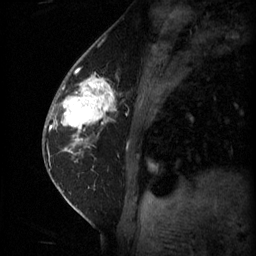
Breast MRI (dynamic contrast-enhanced), one sagittal slice; position 22 of 60 along the scan axis; 3 images stored at this slice position (order not interpretable as contrast timing); 1.5 T; TE 4.2 ms, TR 11 ms; 2 mm slice thickness; 256 × 256 image matrix, field of view 180 × 180 mm. Female patient, age 62 years.
Annotated regions visible in this slice (semi-automatically segmented with operator editing):
- analysis volume of interest (the breast-tissue region the enhancement analysis was run in; not a lesion): bounding box (x1, y1, x2, y2) in pixels: (55, 72, 121, 135)
- tumour enhancement mask (voxels above the 70 % enhancement threshold inside the analysis volume of interest): (56, 78, 116, 131)